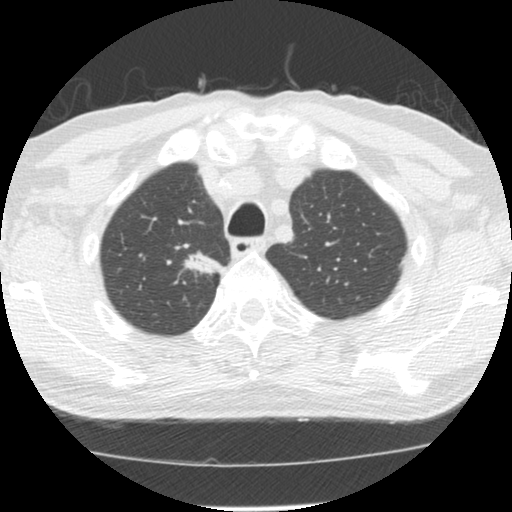
Axial slice from a low-dose chest CT screening exam; baseline annual screen; lung window (W 1500 / L -600 HU); 120 kVp; slice 29 of 139 in the series. Male participant, aged 64 years at enrolment.
Lesion marked by an expert reader, bounding box [x1, y1, x2, y2] px = [175, 237, 223, 279]. Screening reader's record for this exam (one nodule recorded; not confirmed to be the boxed lesion): non-calcified nodule or mass ≥4 mm, right upper lobe, 20 × 13 mm, spiculated (stellate) margins, soft tissue attenuation. Participant outcome: lung cancer diagnosed 73 days after this screen — adenocarcinoma, NOS, right upper lobe, moderately differentiated (G2), stage IA (AJCC 6th edition), 17 mm at pathology.